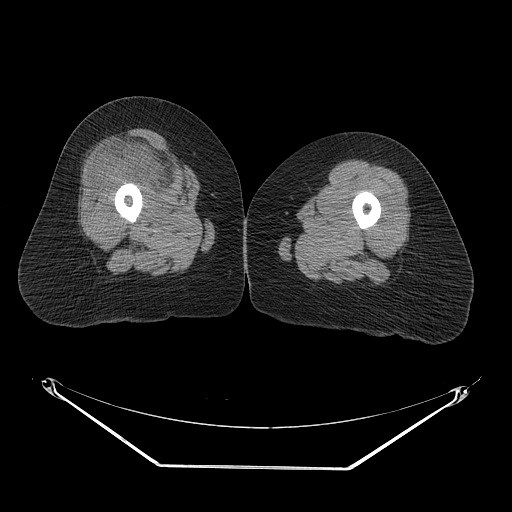
CT of an extremity soft-tissue mass (from a PET/CT study), one axial slice. Slice 25 of 267 in the series (ordered by position). Reconstruction kernel STANDARD. 140 kVp. Soft-tissue window (W 400 / L 40 HU). 512 × 512 image matrix, field of view 500 × 500 mm. Female patient. Case-level facts recorded for this patient, not image findings: histological type: malignant solitary fibrous tumor; grade: intermediate; site of the primary tumour: right thigh.
Structures marked on this image (expert contour drawn on MRI and transferred to this co-registered scan by the dataset authors):
- gross tumour volume including surrounding oedema: bounding box [x1, y1, x2, y2] px = [103, 130, 200, 202]
- gross tumour volume (mass): [110, 141, 181, 193]